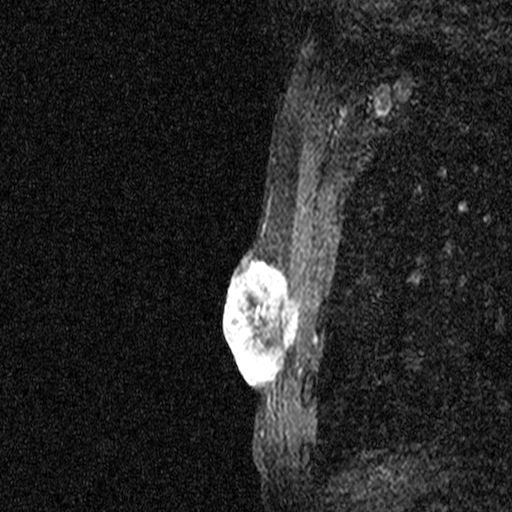
Breast MRI (dynamic contrast-enhanced), one sagittal slice; position 33 of 44 along the scan axis; dynamic contrast-enhanced study with each time point stored as its own series, time point 2 of 3 at this slice position (early post-contrast, ordered by acquisition time); 1.5 T; TE 4.5 ms, TR 11 ms; 2.05 mm slice thickness; 512 × 512 image matrix, field of view 200 × 200 mm. Female patient, age 44 years. Case-level facts recorded for this patient, not image findings: setting: breast cancer imaged before/during neoadjuvant chemotherapy; receptor status: HR-positive, HER2-negative.
Annotated regions visible in this slice (semi-automatically segmented with operator editing):
- analysis volume of interest (the breast-tissue region the enhancement analysis was run in; not a lesion): bounding box (x1, y1, x2, y2) in pixels: (204, 254, 303, 401)
- tumour enhancement mask (voxels above the 90 % enhancement threshold inside the analysis volume of interest): (223, 258, 299, 400)